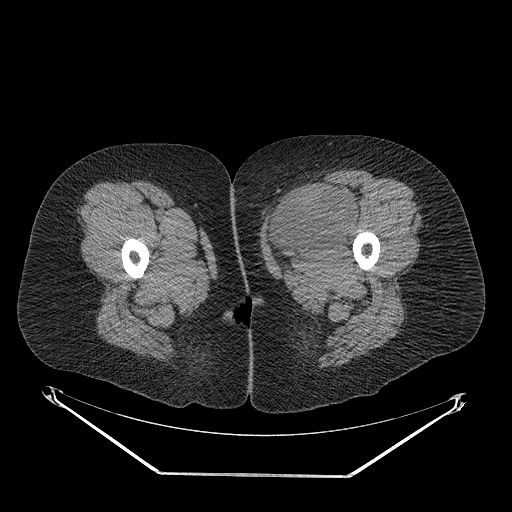
CT of an extremity soft-tissue mass (from a PET/CT study), one axial slice. Slice 29 of 267 in the series (ordered by position). Reconstruction kernel STANDARD. 140 kVp. Soft-tissue window (W 400 / L 40 HU). 3.75 mm slice thickness. 512 × 512 image matrix, field of view 500 × 500 mm. Female patient. From the clinical record (not read from this slice): histological type: myxofibrosarcoma; grade: intermediate; site of the primary tumour: left thigh.
Annotated regions visible in this slice (expert contour drawn on MRI and transferred to this co-registered scan by the dataset authors):
- gross tumour volume including surrounding oedema: bounding box [x1, y1, x2, y2] px = [265, 187, 359, 261]
- gross tumour volume (mass): [267, 187, 355, 252]